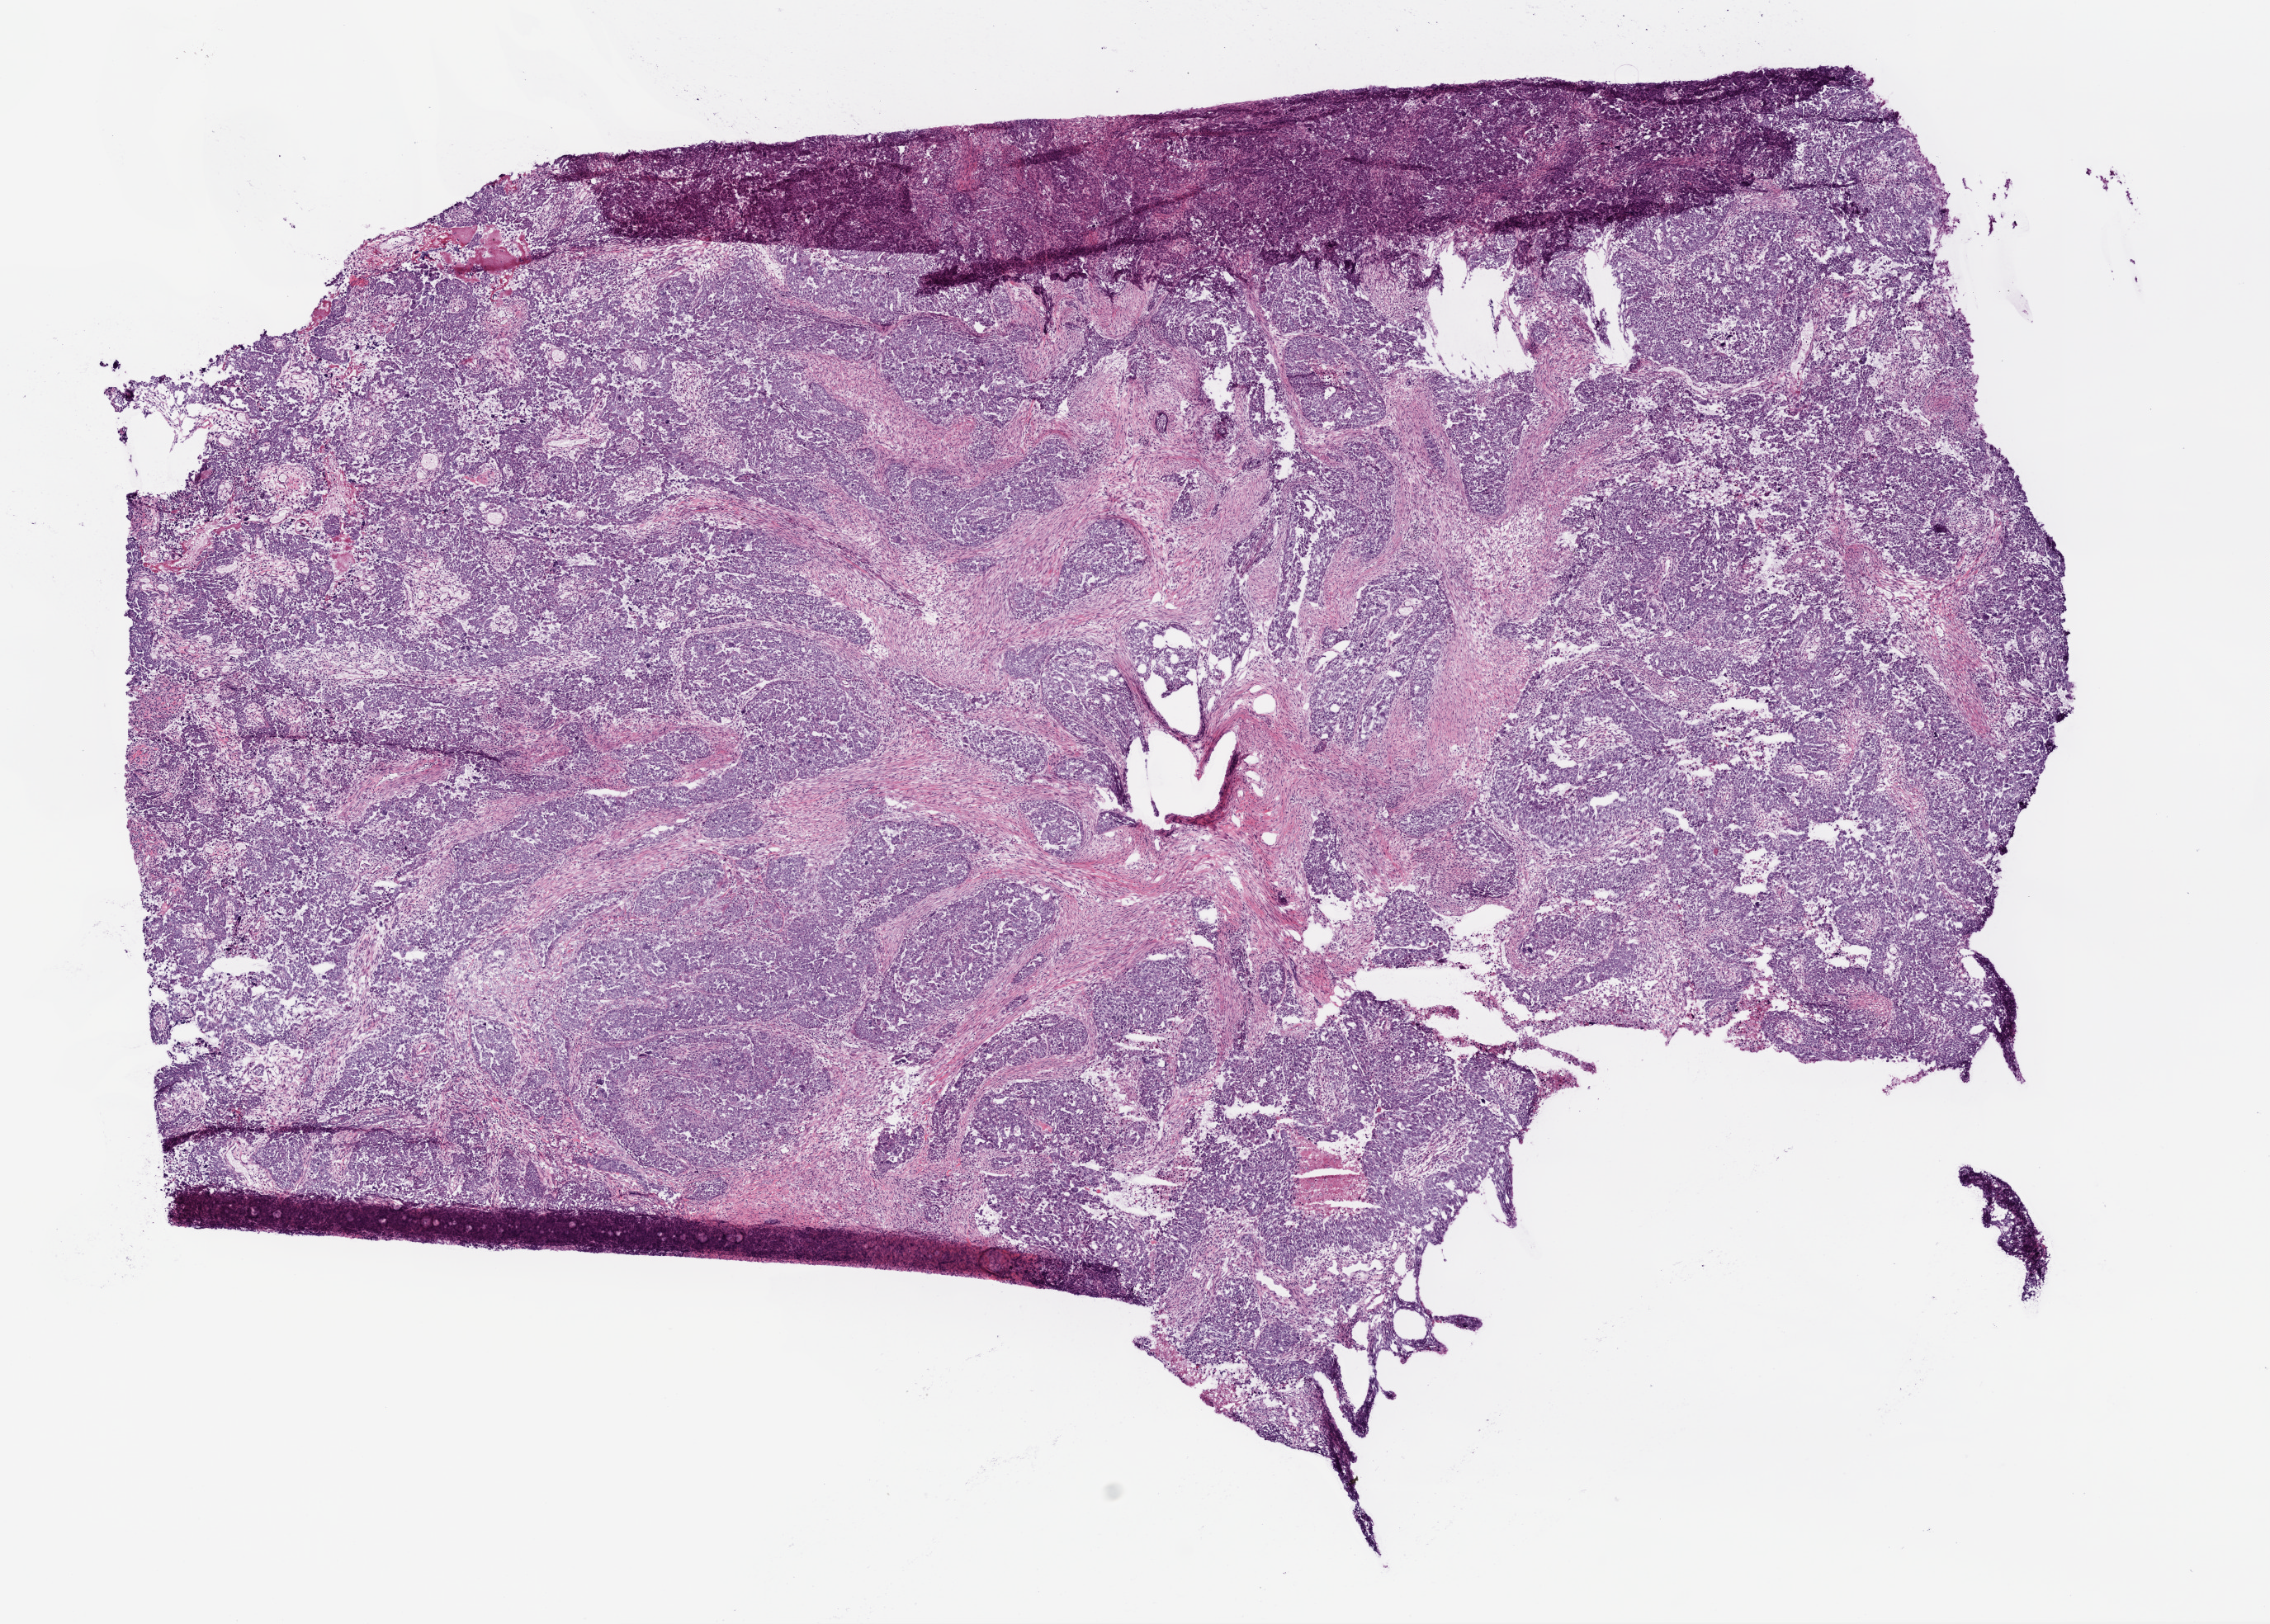
Digitized Hematoxylin and eosin (H&E) stained tissue section (whole slide) — whole scanned area (about 11.0 x 7.9 mm, acquisition: 20x scan) shown as a low-resolution overview. Frozen section. Primary tumour sample from the ovary. Female patient; age at initial diagnosis 54 years.
Pathologic diagnosis: Serous cystadenocarcinoma, NOS.